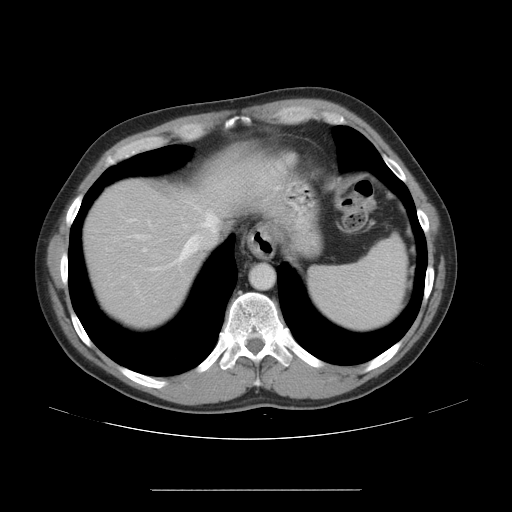
Contrast-enhanced abdominal CT, one axial slice; slice 38 of 48 in the series (ordered by position); 120 kVp; intravenous contrast given; soft-tissue window (W 400 / L 40 HU); 5 mm slice thickness; 512 × 512 image matrix, field of view 409 × 409 mm. Male patient, age 56 years. Case-level facts recorded for this patient, not image findings: diagnosis: colorectal cancer liver metastases, imaged before liver resection; multiple liver metastases: yes; largest metastasis: 1.8 cm; chemotherapy before resection: yes.
Structures marked on this image (manually delineated by an expert):
- hepatic veins: bounding box (x1, y1, x2, y2) in pixels: (170, 212, 218, 266)
- liver: (84, 182, 201, 327)
- planned liver remnant (the part of the liver to remain after resection): (84, 183, 201, 327)
- portal vein (with intrahepatic branches): (129, 219, 136, 222)